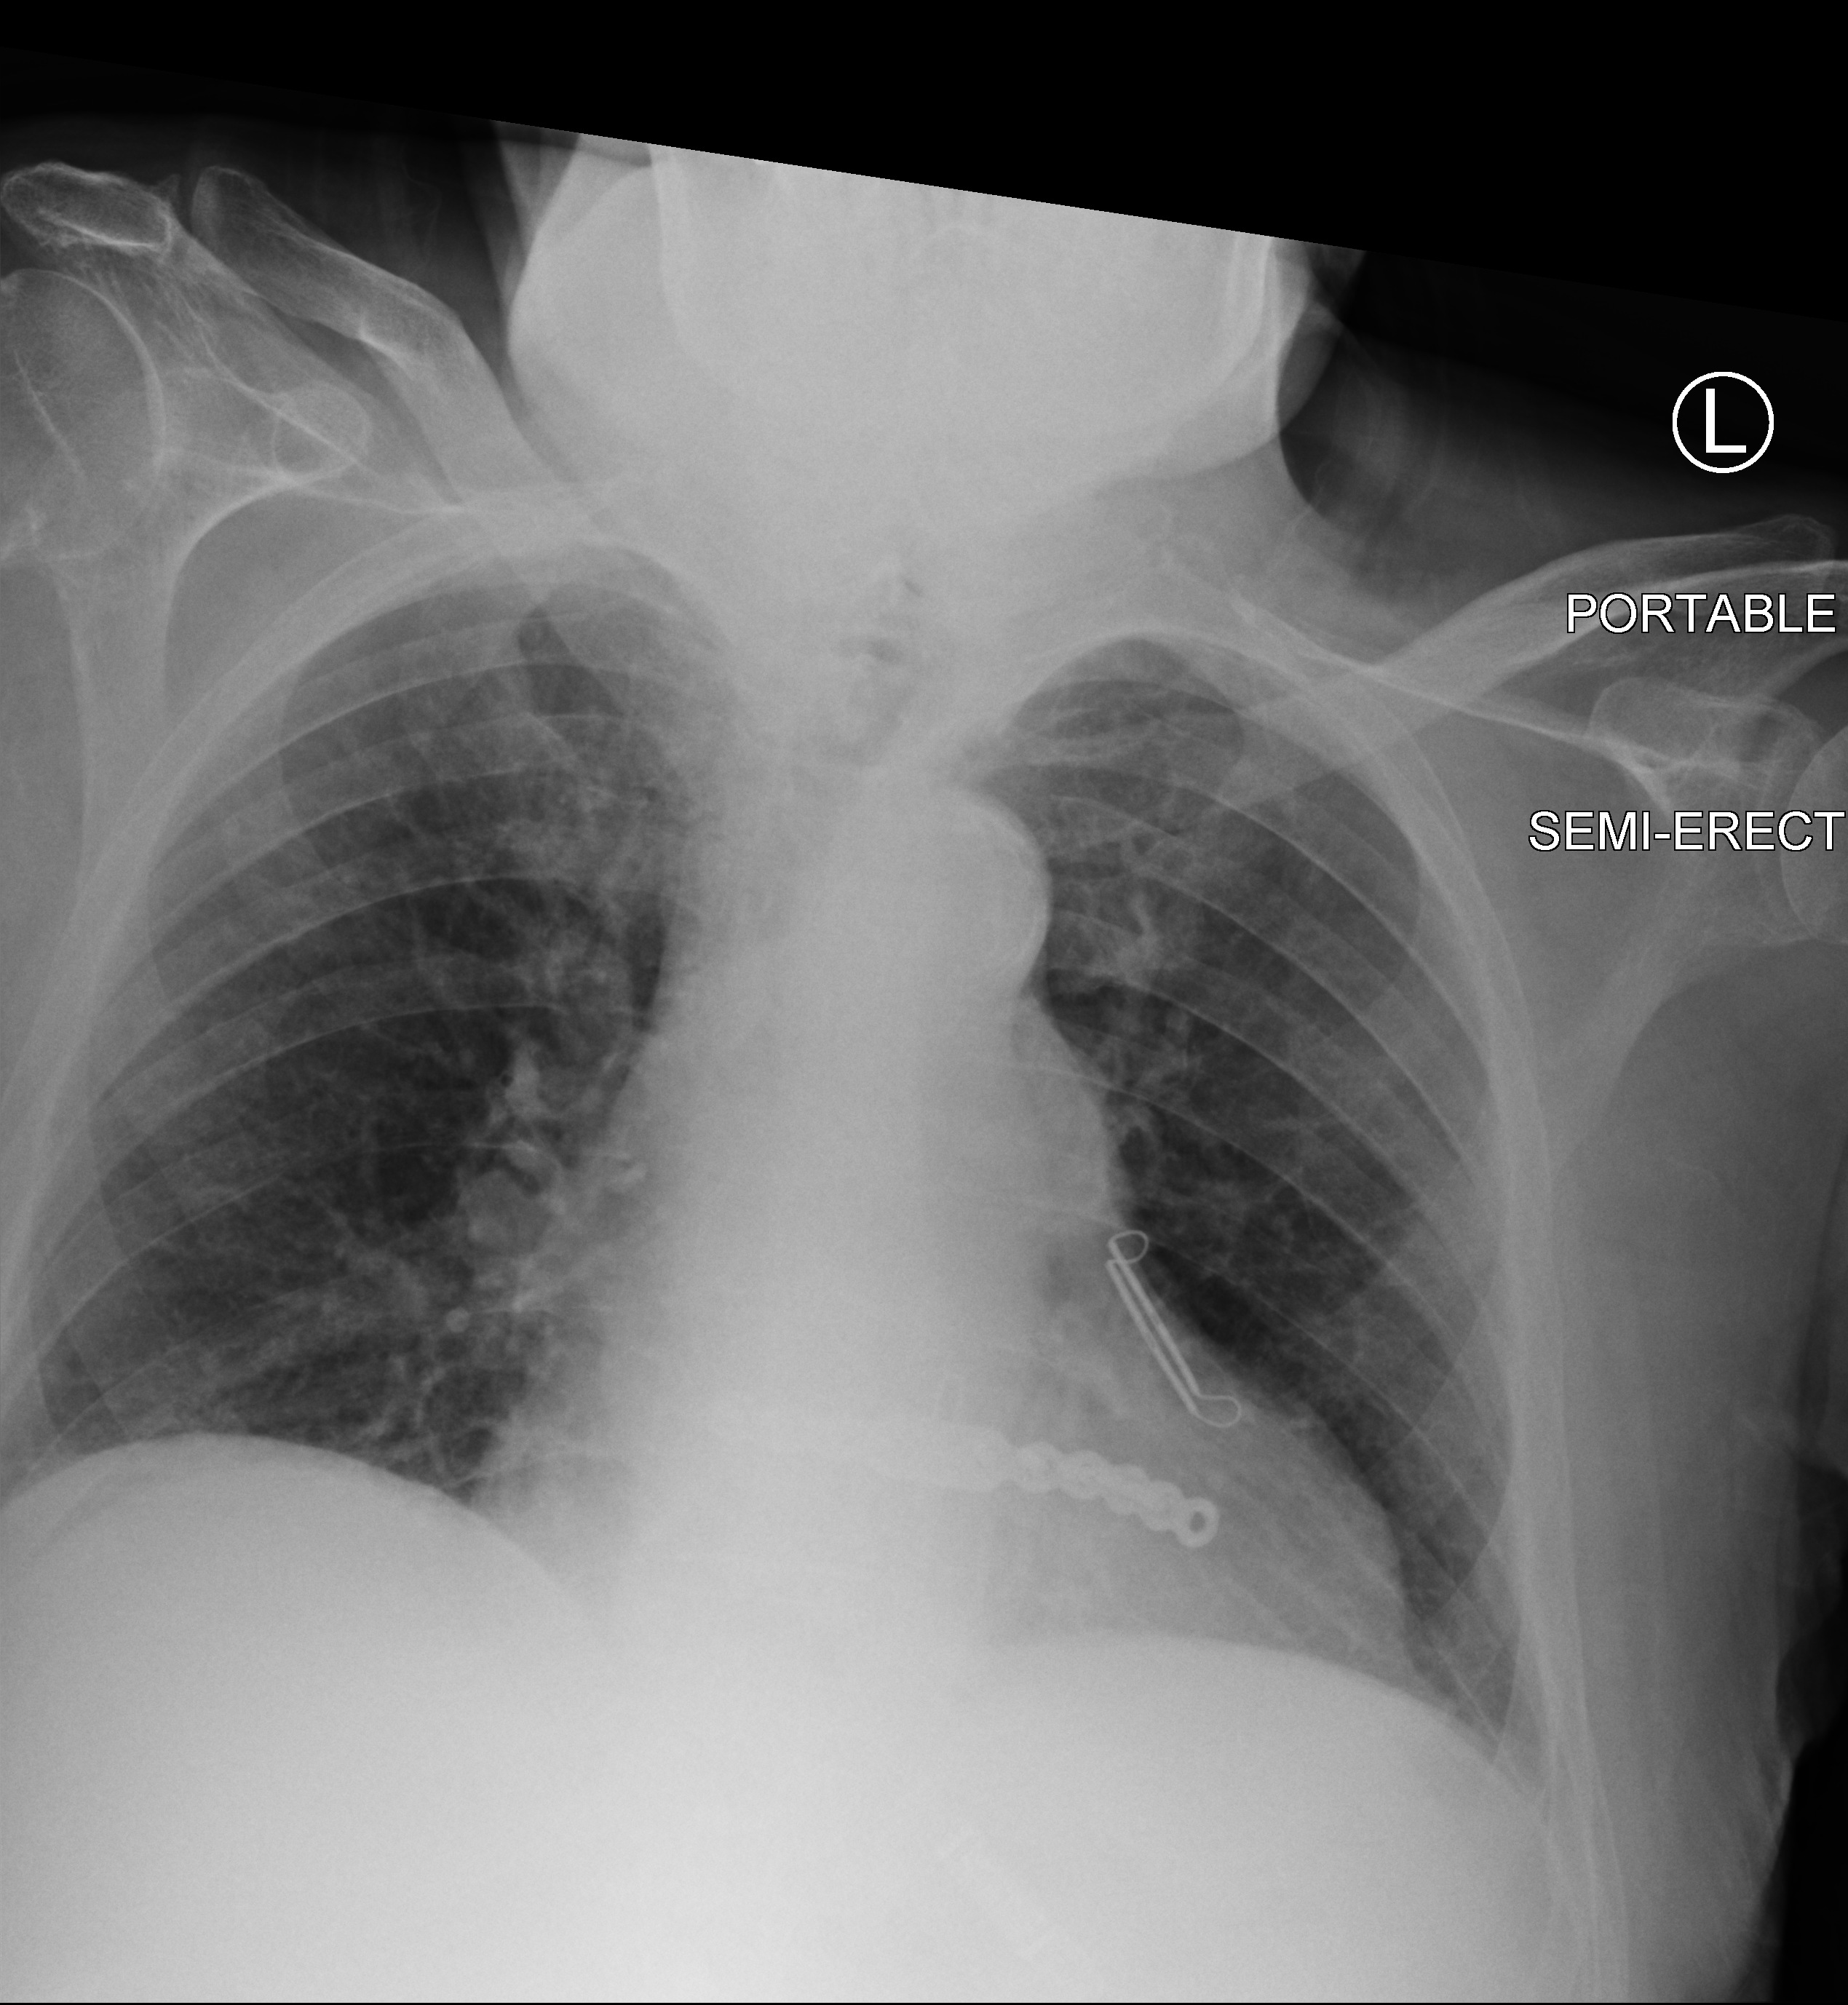
Bedside chest radiograph (computed radiography). Patient hospitalised with COVID-19; male, aged 75–90 years.
Admission-level facts for this patient (not findings on this image; timing relative to this image not recorded):
- mechanically ventilated during this hospital stay: no
- diabetes (admission record): yes
- length of hospital stay: 4 days